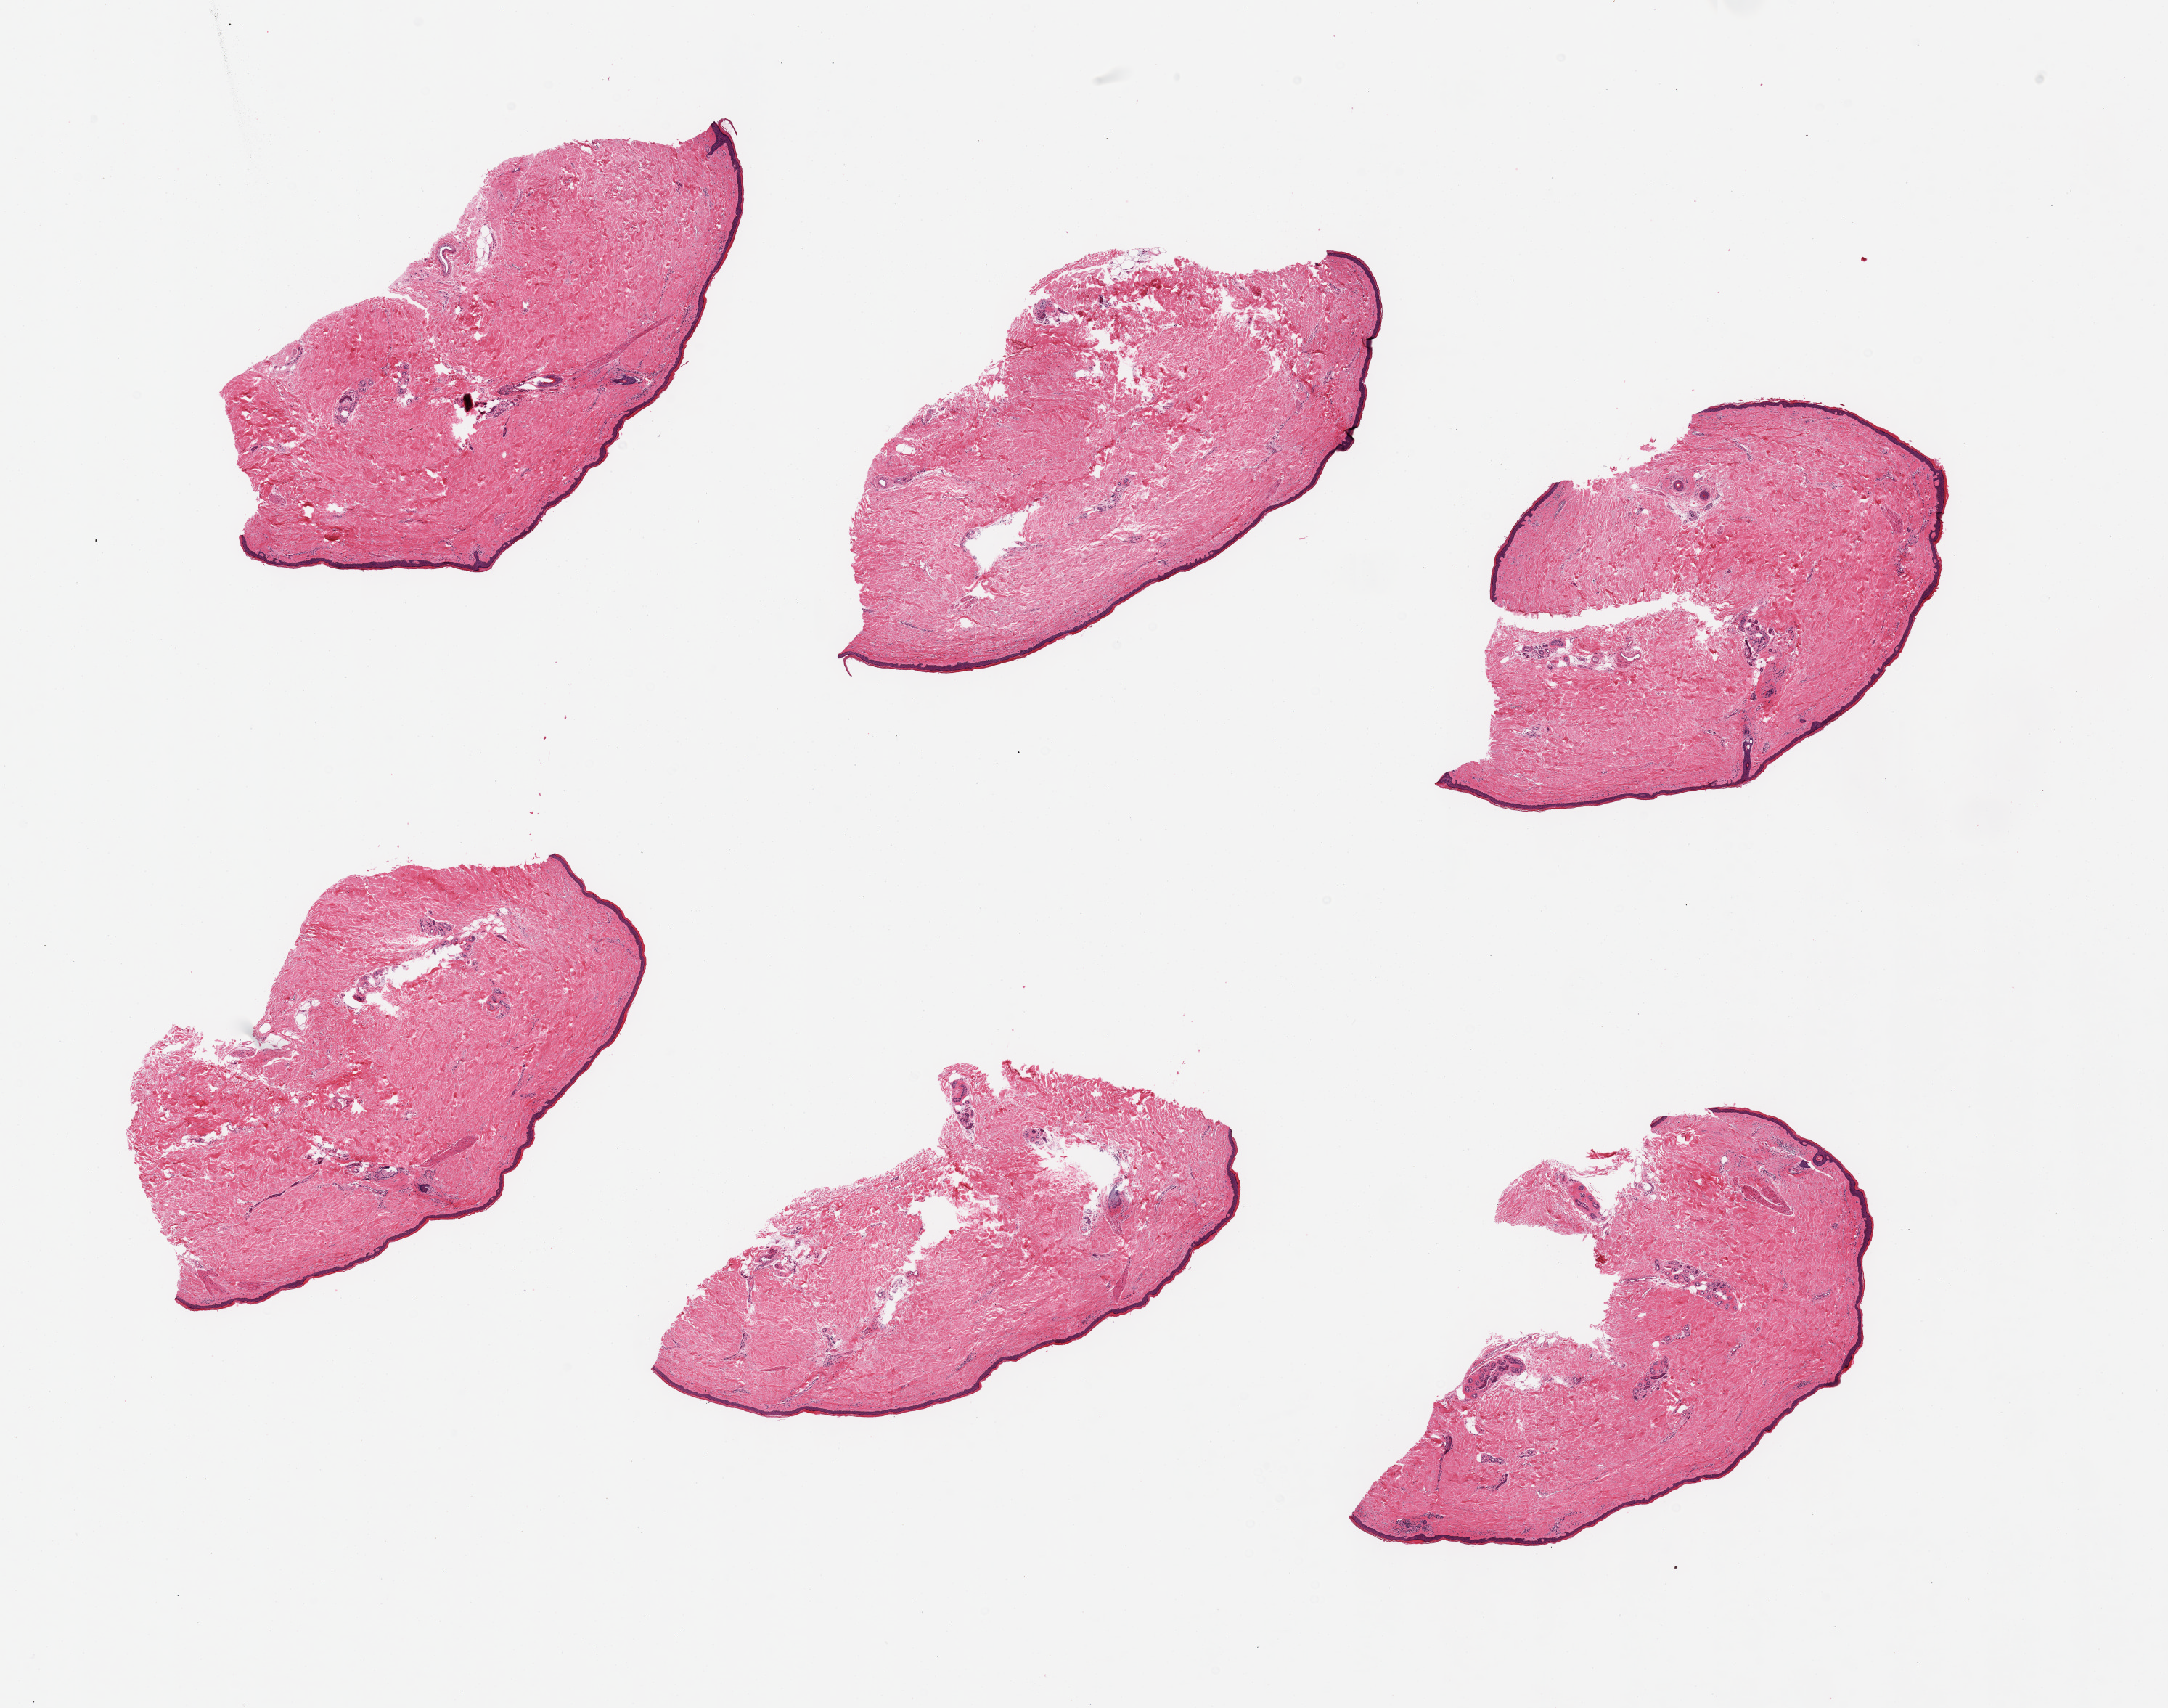
Digitized hematoxylin and eosin (H&E)-stained section — a low-resolution overview of the entire scanned area, about 23.6 x 18.6 mm, PAXgene-fixed paraffin-embedded (PFPE) section, sampled site (target tissue): skin of lower leg, tissue donor sample.
- reviewer comment on this tissue sample: 6 pieces; trace dermal fat; squamous epithelium is ~35-40 microns